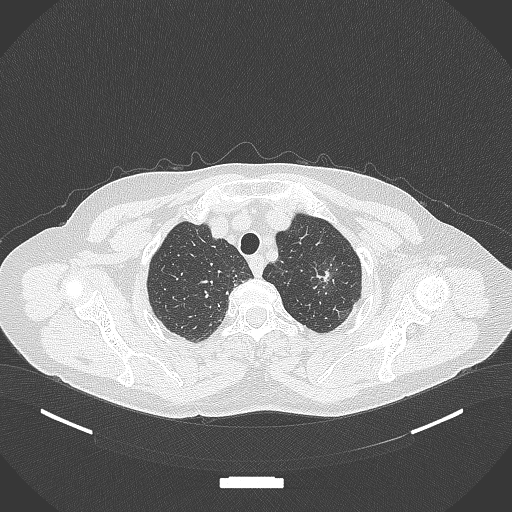
Chest CT, one axial slice; slice 312 of 369 in the series (ordered by position); reconstruction kernel B70f; 120 kVp; lung window (W 1500 / L -600 HU); 512 × 512 image matrix, field of view 400 × 400 mm. Female patient, age 64 years. From the clinical record (not read from this slice): clinical TNM (as recorded): T1c N0 M0.
Outlined on this slice (bounding box drawn by a radiologist):
- lung tumour (recorded histology: adenocarcinoma): bounding box (x1, y1, x2, y2) in pixels: (305, 253, 346, 300)